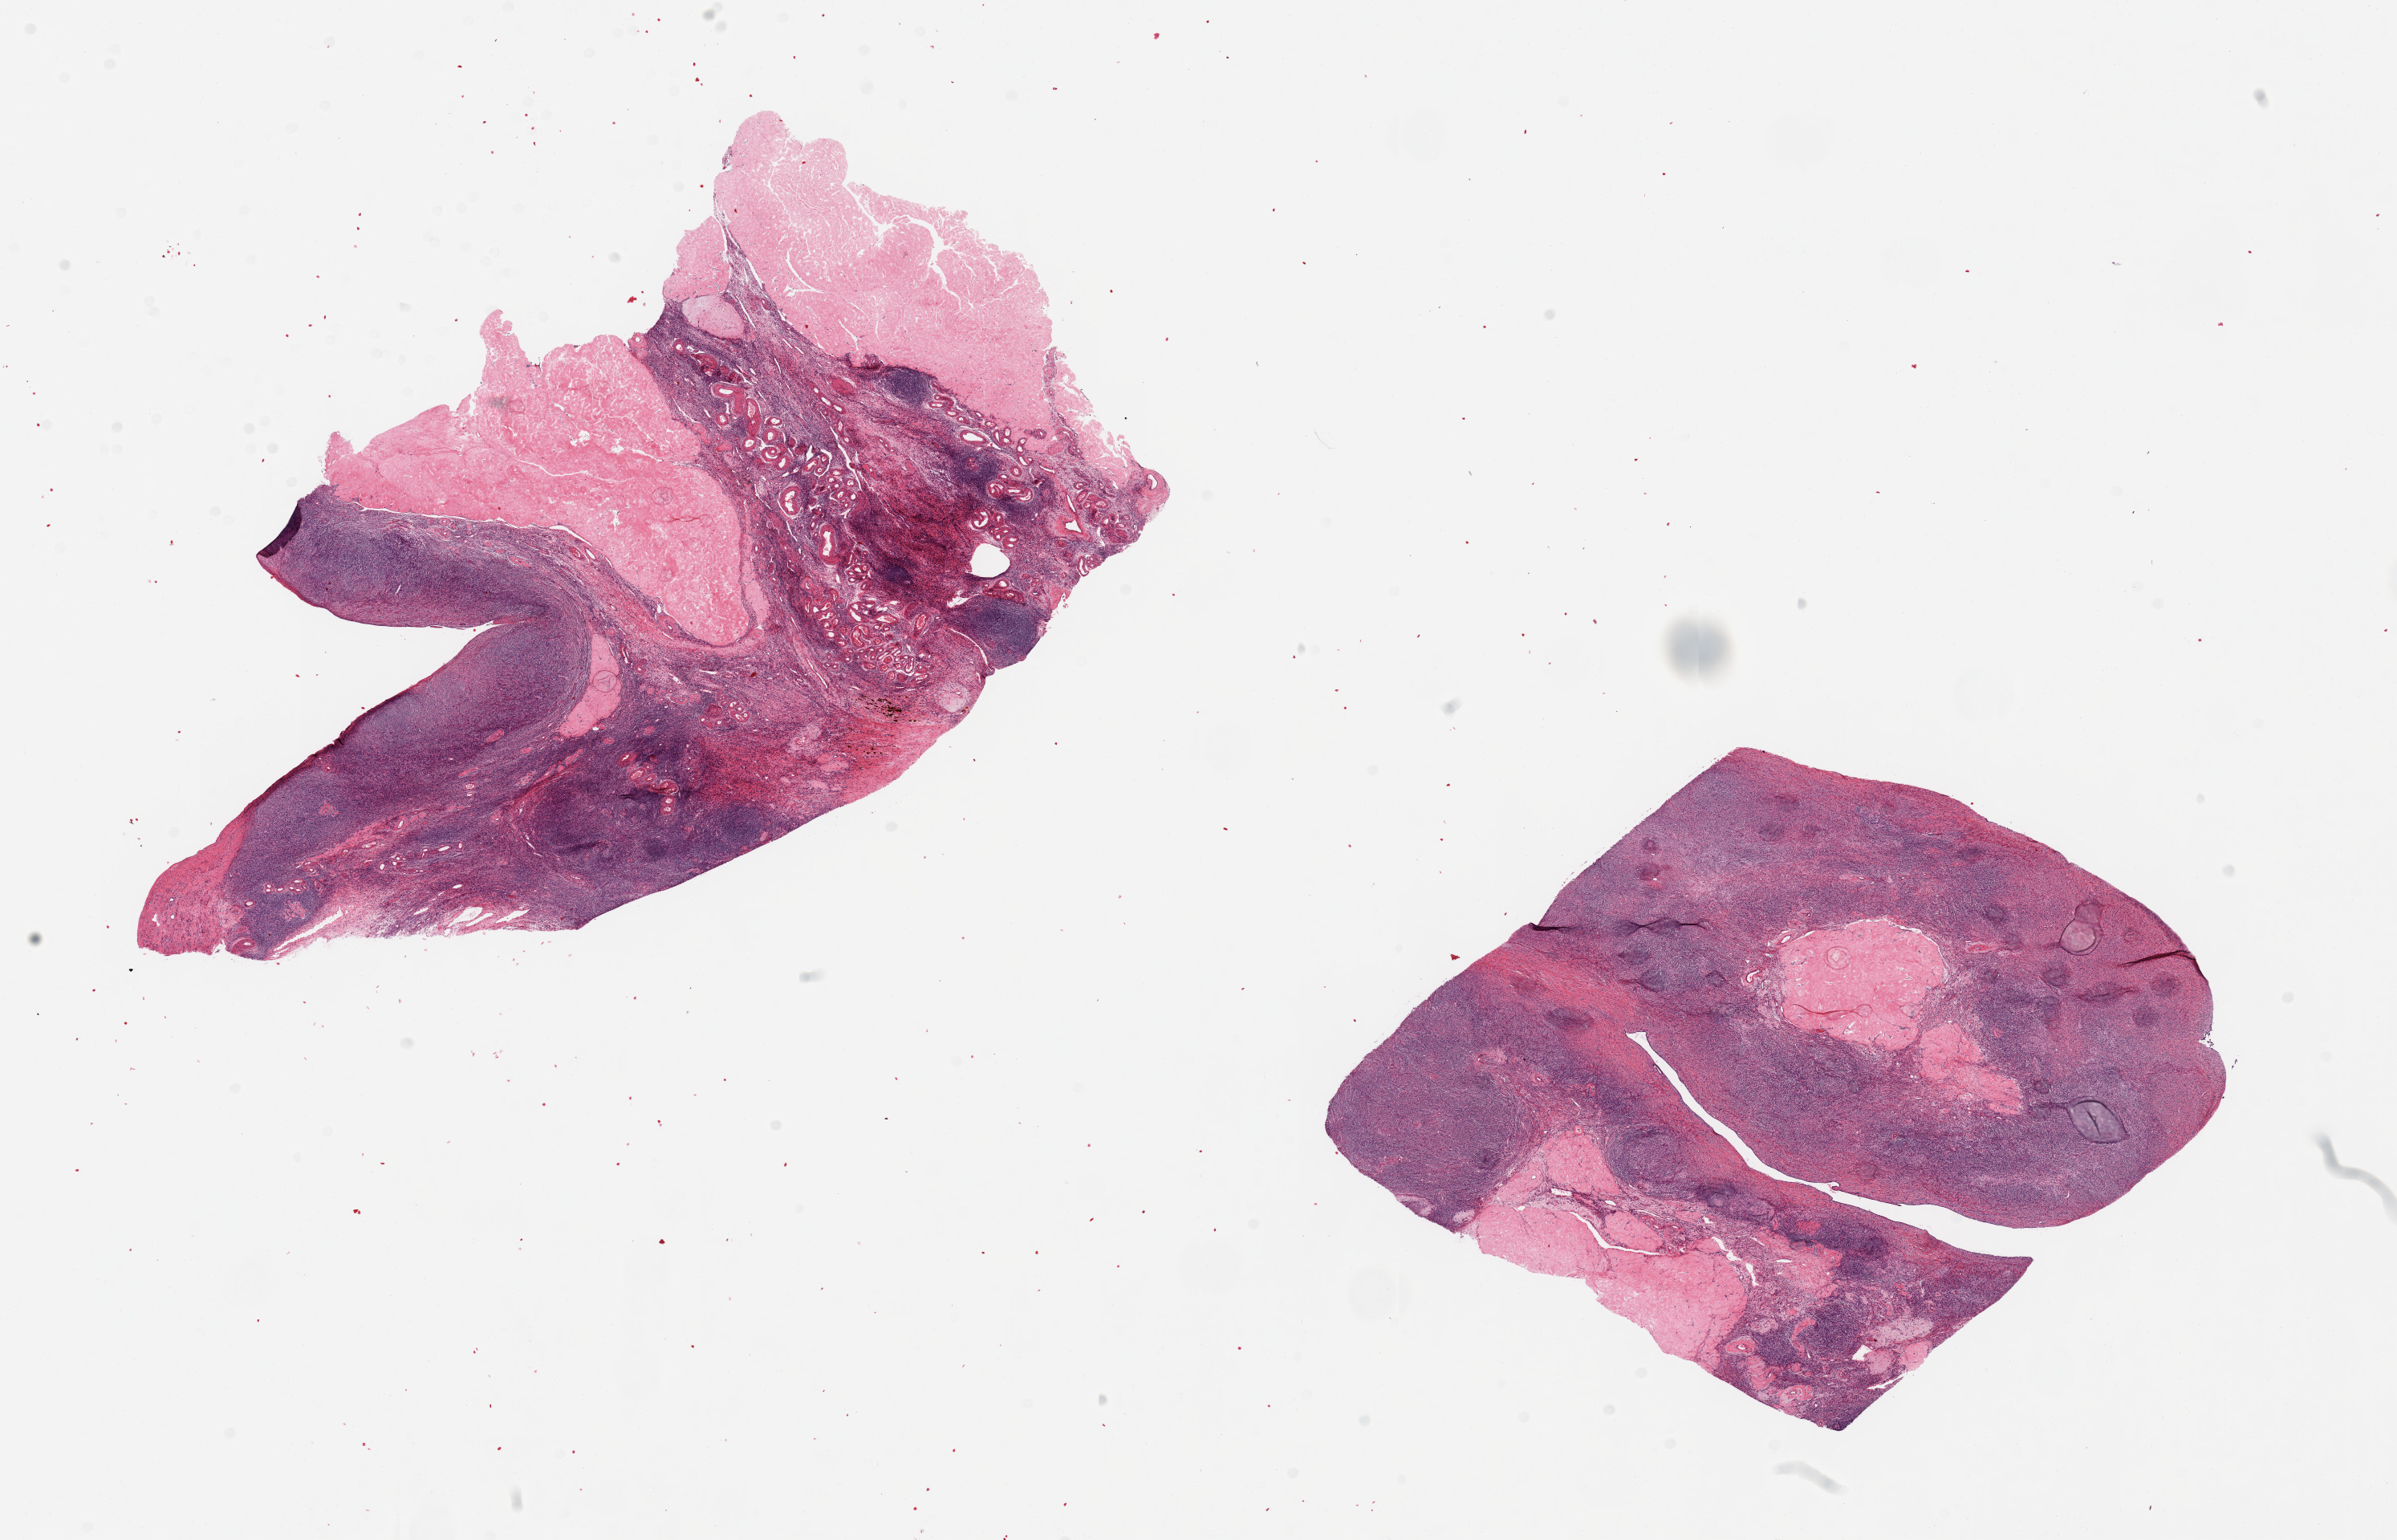
Digitized H&E-stained section, brightfield, a low-resolution overview of the entire scanned area, about 23.6 x 15.2 mm. PAXgene-fixed paraffin-embedded (PFPE) section. Section of ovary (target tissue). Donor tissue sample. Donor: female.
Pathologist's review note for this sample: 2 pieces; atrophic with corpora albicantia occupying 40 & 20%.